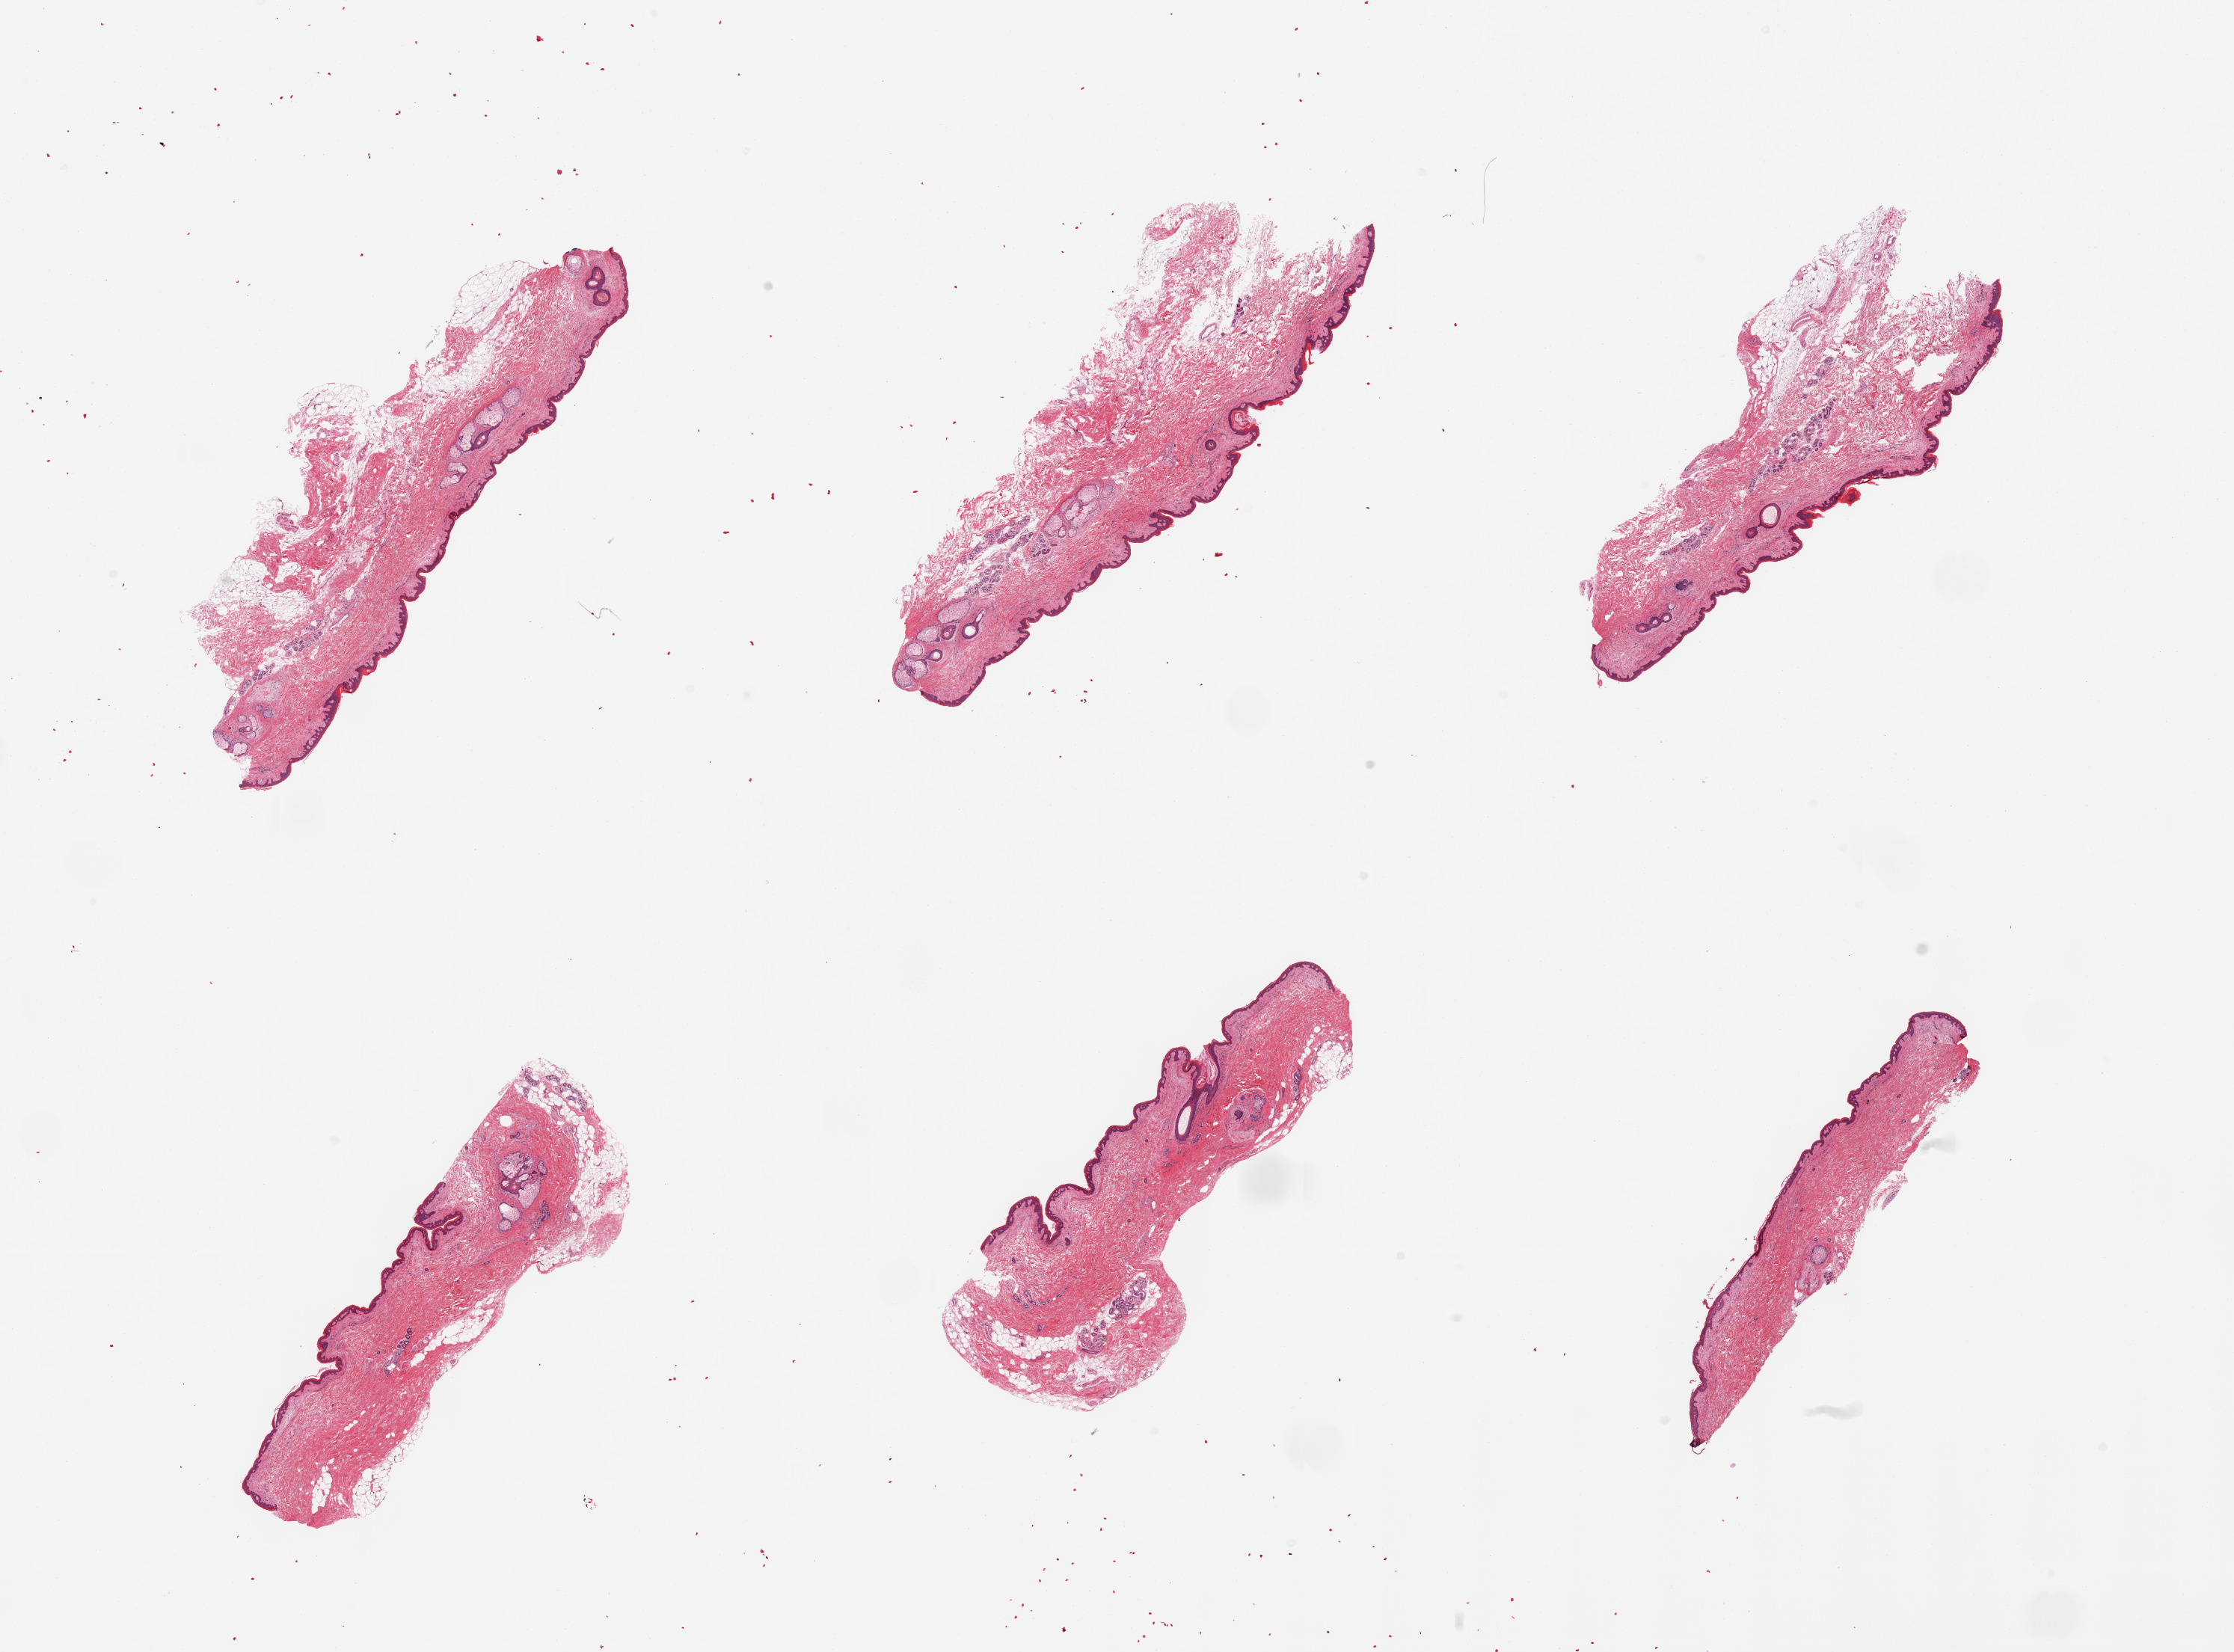
Whole-slide image, haematoxylin and eosin stain, a low-resolution overview of the entire scanned area, about 23.6 x 17.5 mm (acquisition: 20x scan). PAXgene-fixed, paraffin-embedded tissue. Target tissue: skin of suprapubic region. Tissue donor sample. Donor sex: male.
• pathologist's review note for this sample: 6 pieces, squamous epithelium is ~40-50 microns, minimal dermal fat